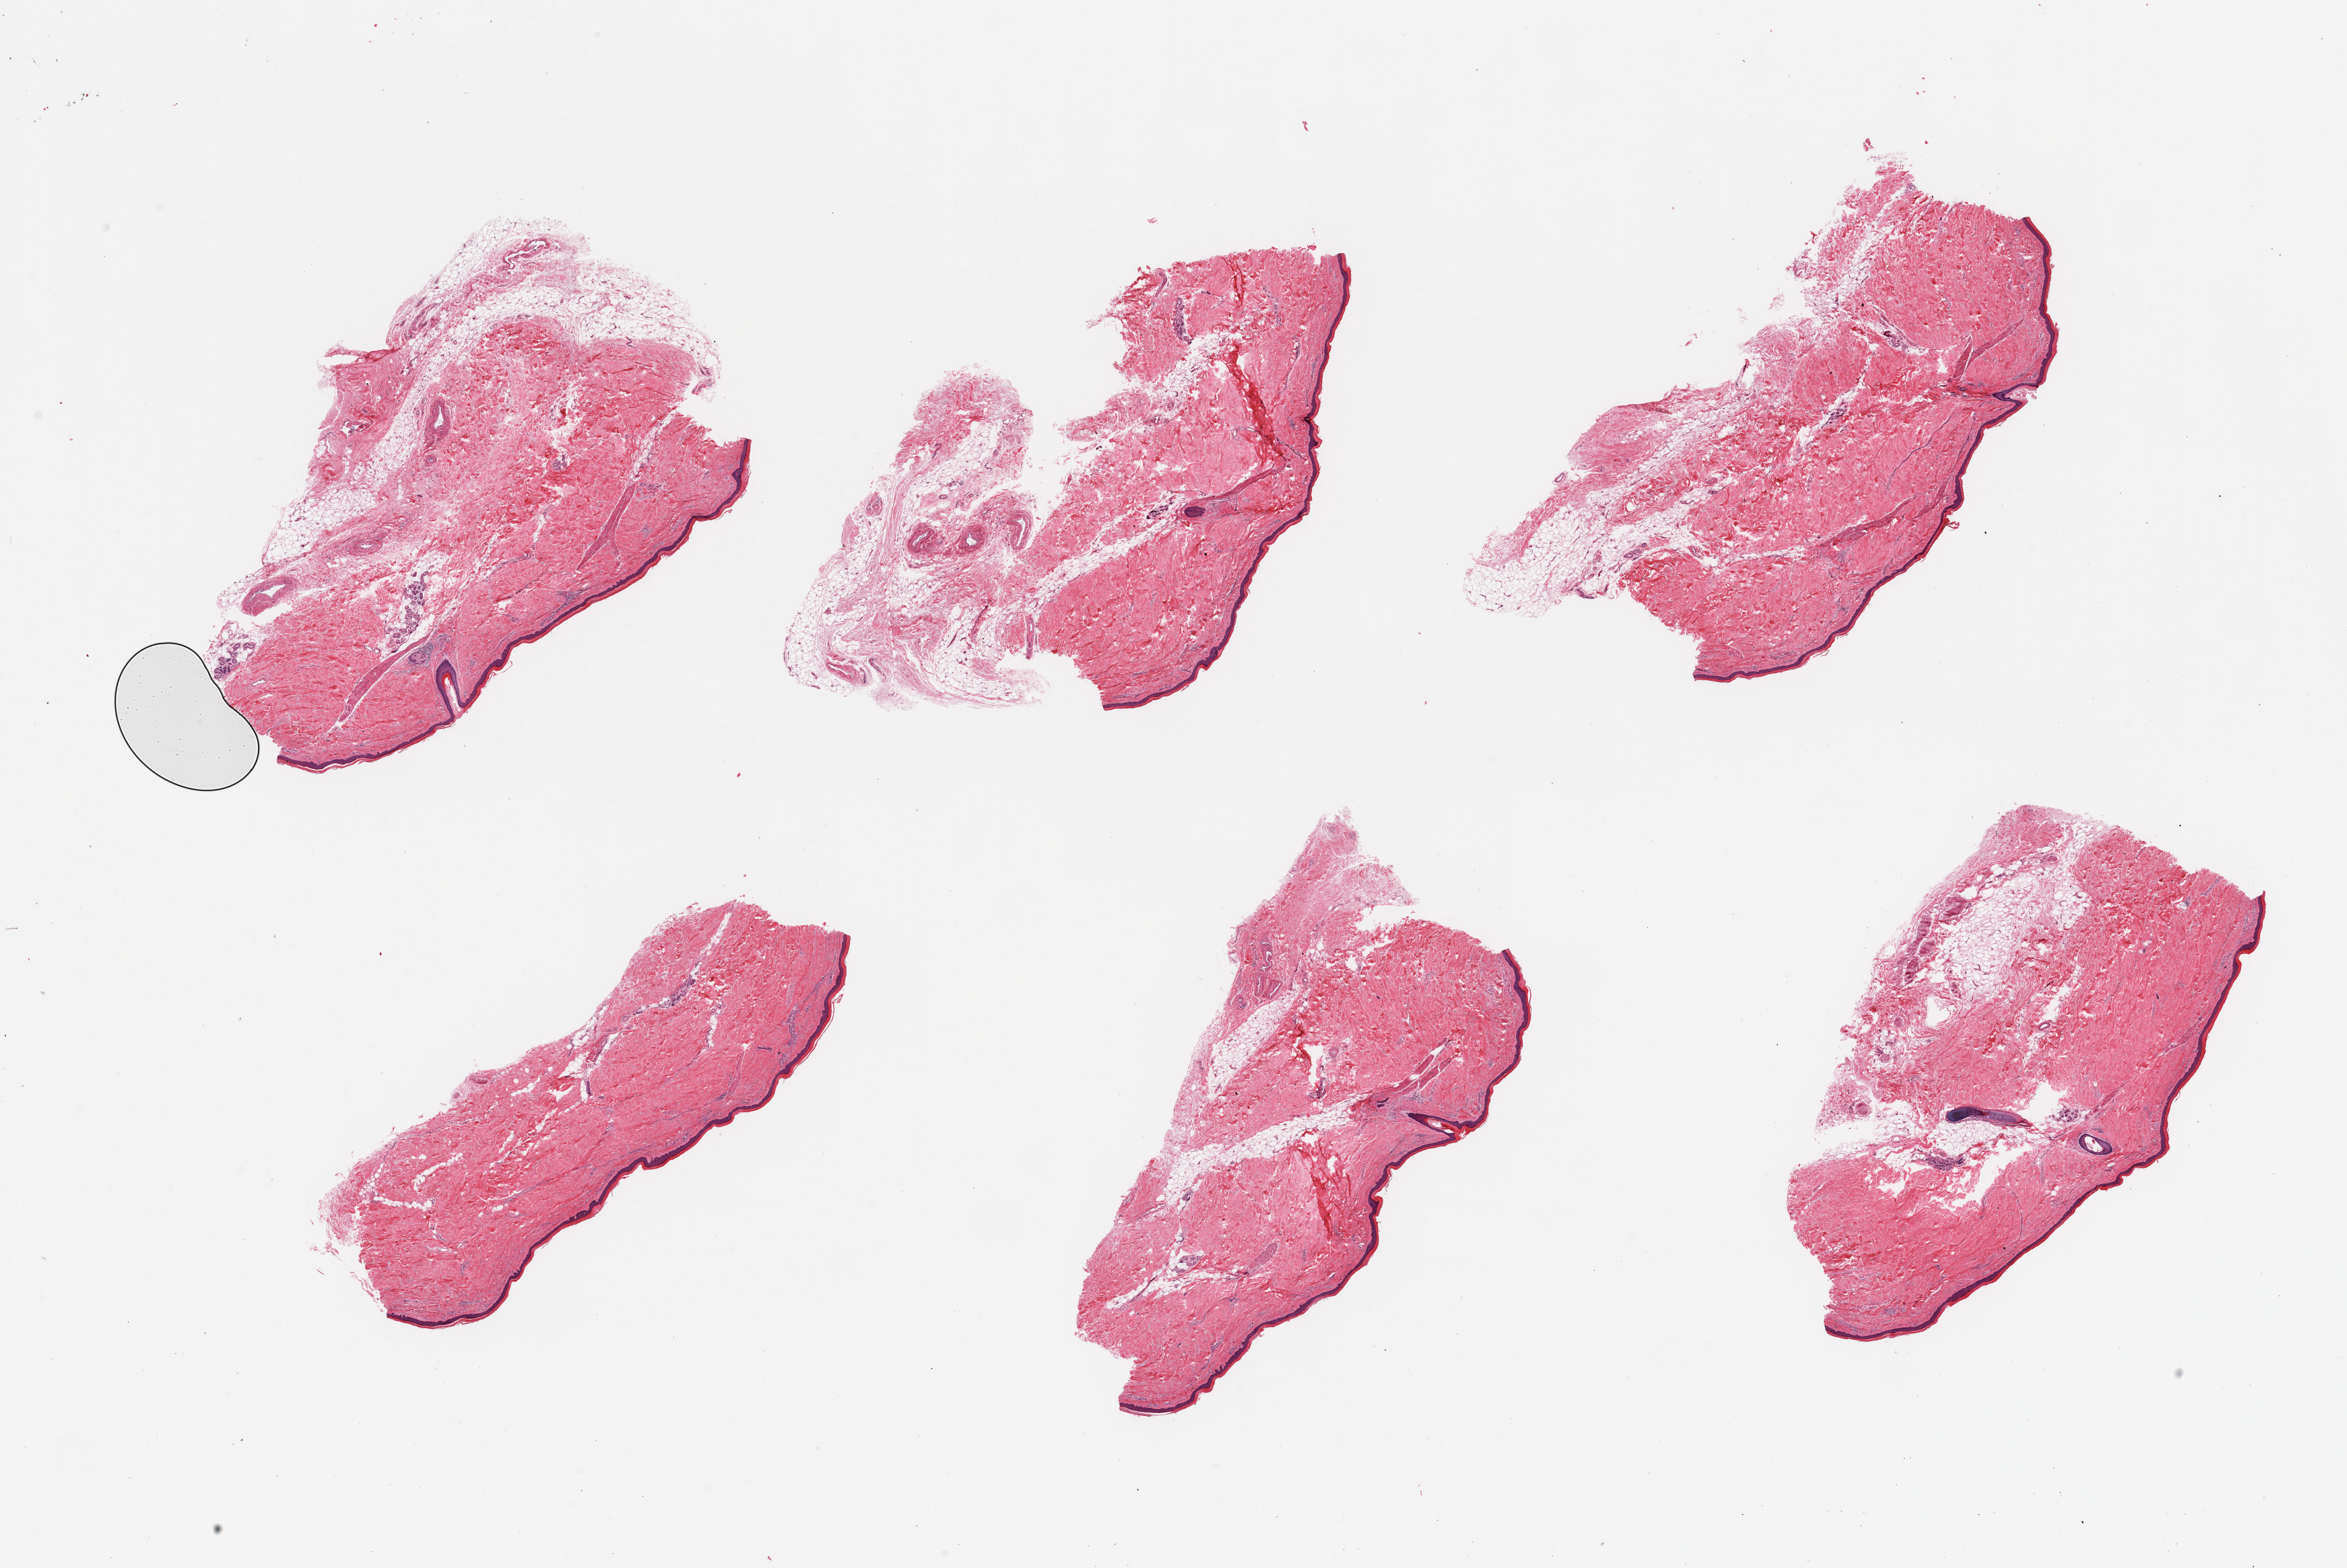
Digitized hematoxylin and eosin (H&E)-stained section — a low-resolution overview of the entire scanned area, about 27.6 x 18.4 mm. PAXgene-fixed paraffin-embedded (PFPE) section. Sampled site (target tissue): skin of lower leg. Tissue donor sample.
Review note (as recorded): 6 pieces; up to 30% subcutaneous tissue.